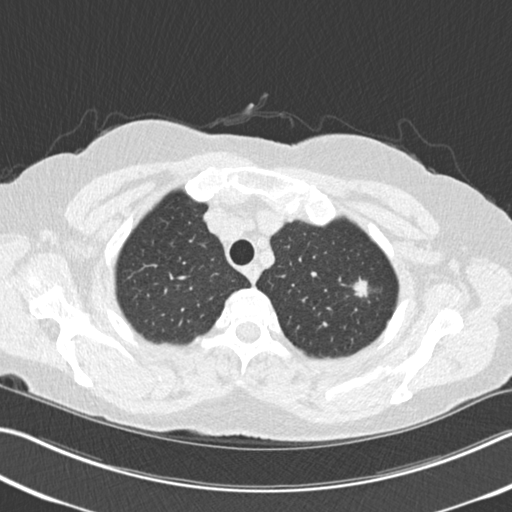
Low-dose screening chest CT, one axial slice; position 192 of 225 along the scan axis; reconstruction kernel B30f; lung window (W 1500 / L -600 HU); 2 mm slice thickness; 512 × 512 image matrix, field of view 342 × 342 mm.
Annotated regions visible in this slice (expert manual segmentation):
- lesion 1 (tumor): bounding box [x1, y1, x2, y2] px = [354, 277, 368, 298]